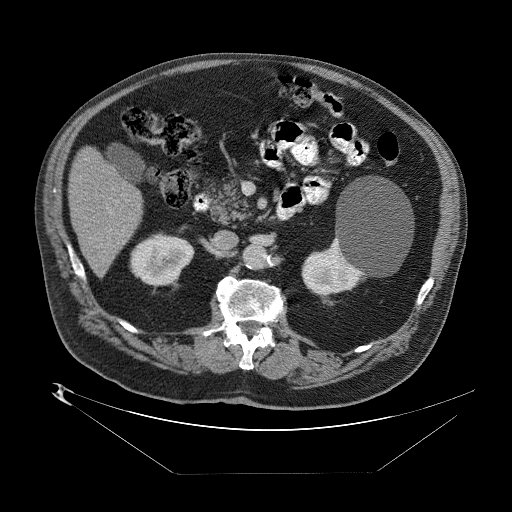
Contrast-enhanced abdominal CT (liver protocol), one axial slice. Slice 24 of 89 in the series (ordered by position). Reconstruction kernel STANDARD. 140 kVp. One of 2 acquisitions stored at this slice position. Soft-tissue window (W 400 / L 40 HU). 2.5 mm slice thickness. 512 × 512 image matrix, field of view 480 × 480 mm. Case-level facts recorded for this patient, not image findings: diagnosis: hepatocellular carcinoma (patient treated with transarterial chemoembolisation; whether this scan precedes or follows treatment is not stated here); TNM stage (as recorded): Stage-II; Child-Pugh class: B; tumour nodularity: multinodular; tumour size: 4 cm.
Structures marked on this image (semi-automatic segmentation, software-assisted and operator-edited):
- abdominal aorta: bounding box <245,246,267,269> (left, top, right, bottom; pixels)
- liver parenchyma outside the tumour (the mass and vessels are separate outlines, so this box may not span the whole liver): <66,142,144,272>
- liver vessels: <86,207,113,254>